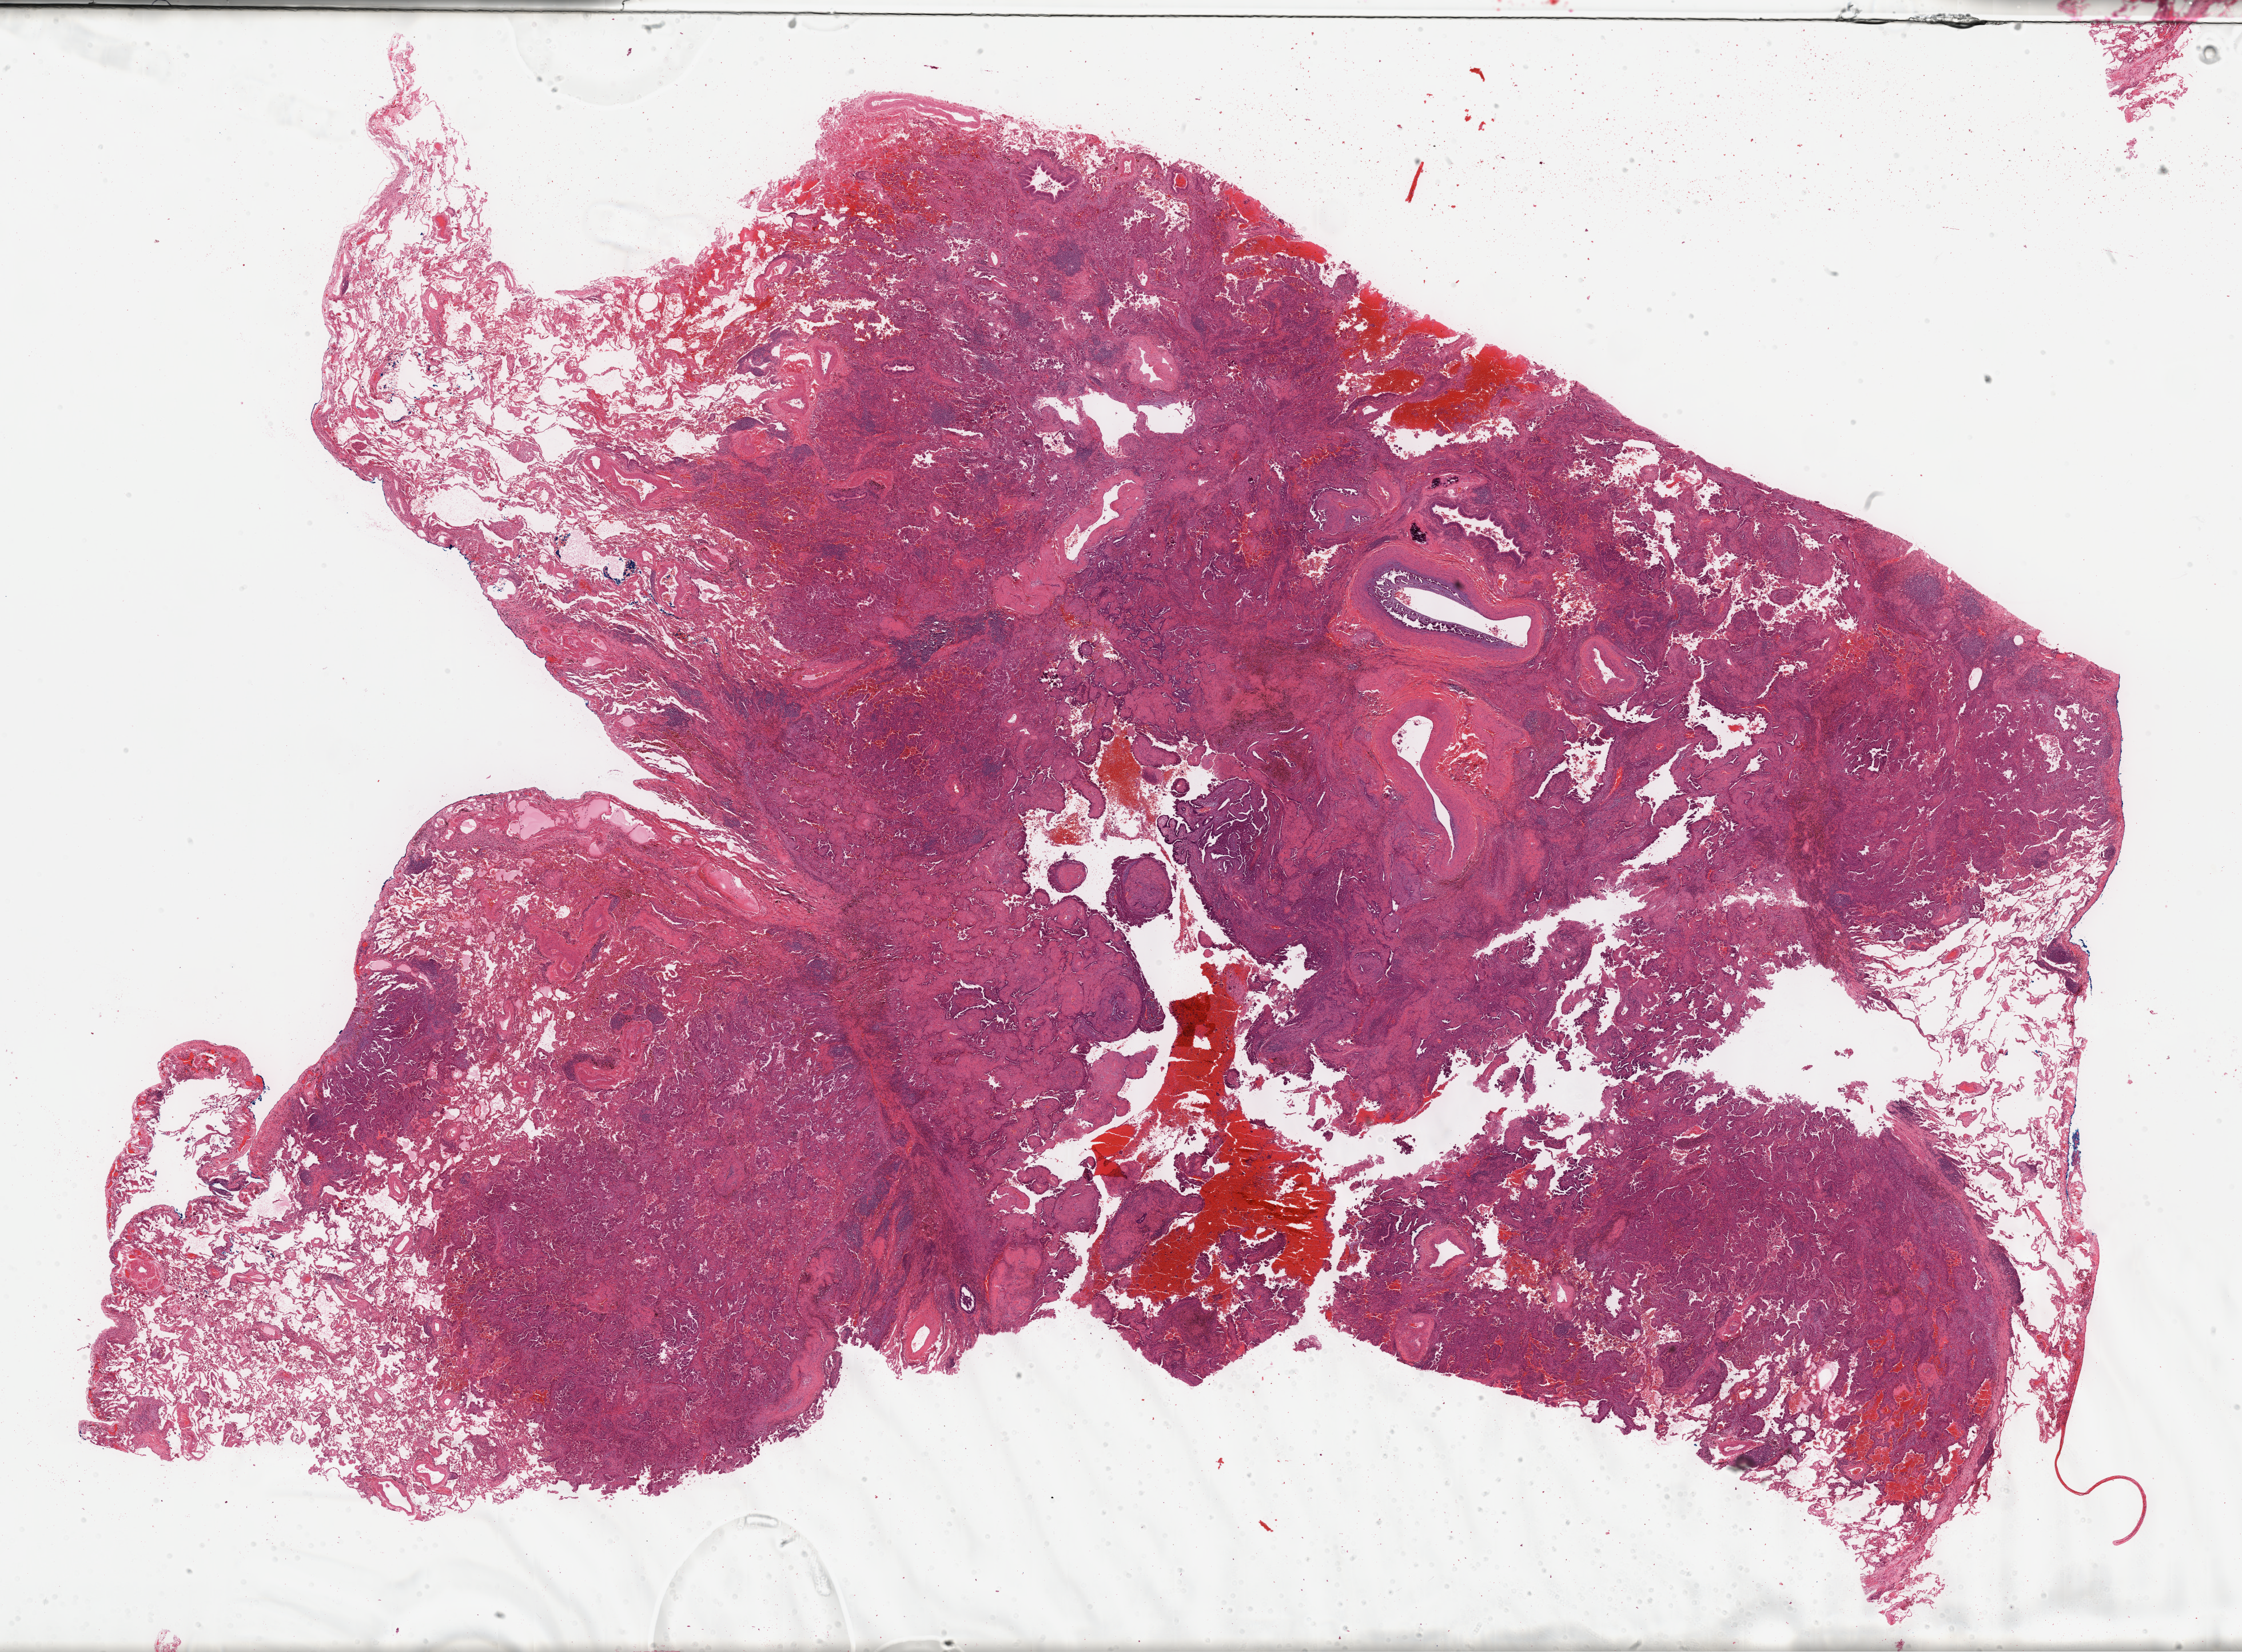
Digitized H&E-stained tissue section (whole slide), a low-resolution overview of the entire scanned area, about 31.7 x 23.4 mm; FFPE section; primary tumour sample from the lung. Male patient; age at initial diagnosis 71 years.
Laterality: left. AJCC pathologic stage: IV (7th edition). Diagnosis: Acinar cell carcinoma (upper lobe, lung). TNM: T2a N0 M1a.